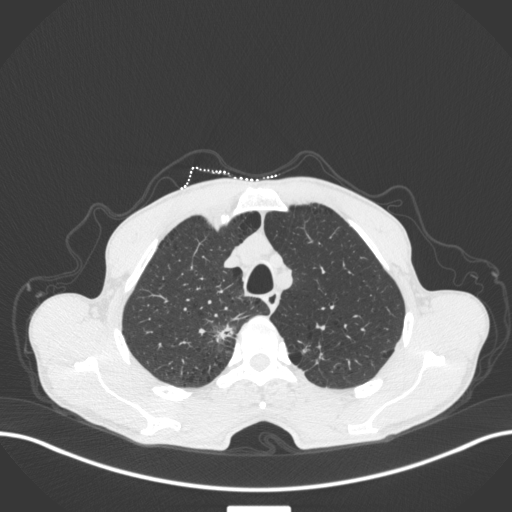
Chest CT, one axial slice; position 348 of 445 along the scan axis; reconstruction kernel B31f; lung window (W 1500 / L -600 HU); 1 mm slice thickness; 512 × 512 image matrix, field of view 400 × 400 mm. Patient: male, 70 years. From the clinical record (not read from this slice): clinical TNM (as recorded): T1a N0 M0; histopathological grade: G1-2.
Structures marked on this image (rectangle marked by the reading radiologist):
- lung tumour (recorded histology: adenocarcinoma): bounding box [x1, y1, x2, y2] px = [209, 323, 235, 345]